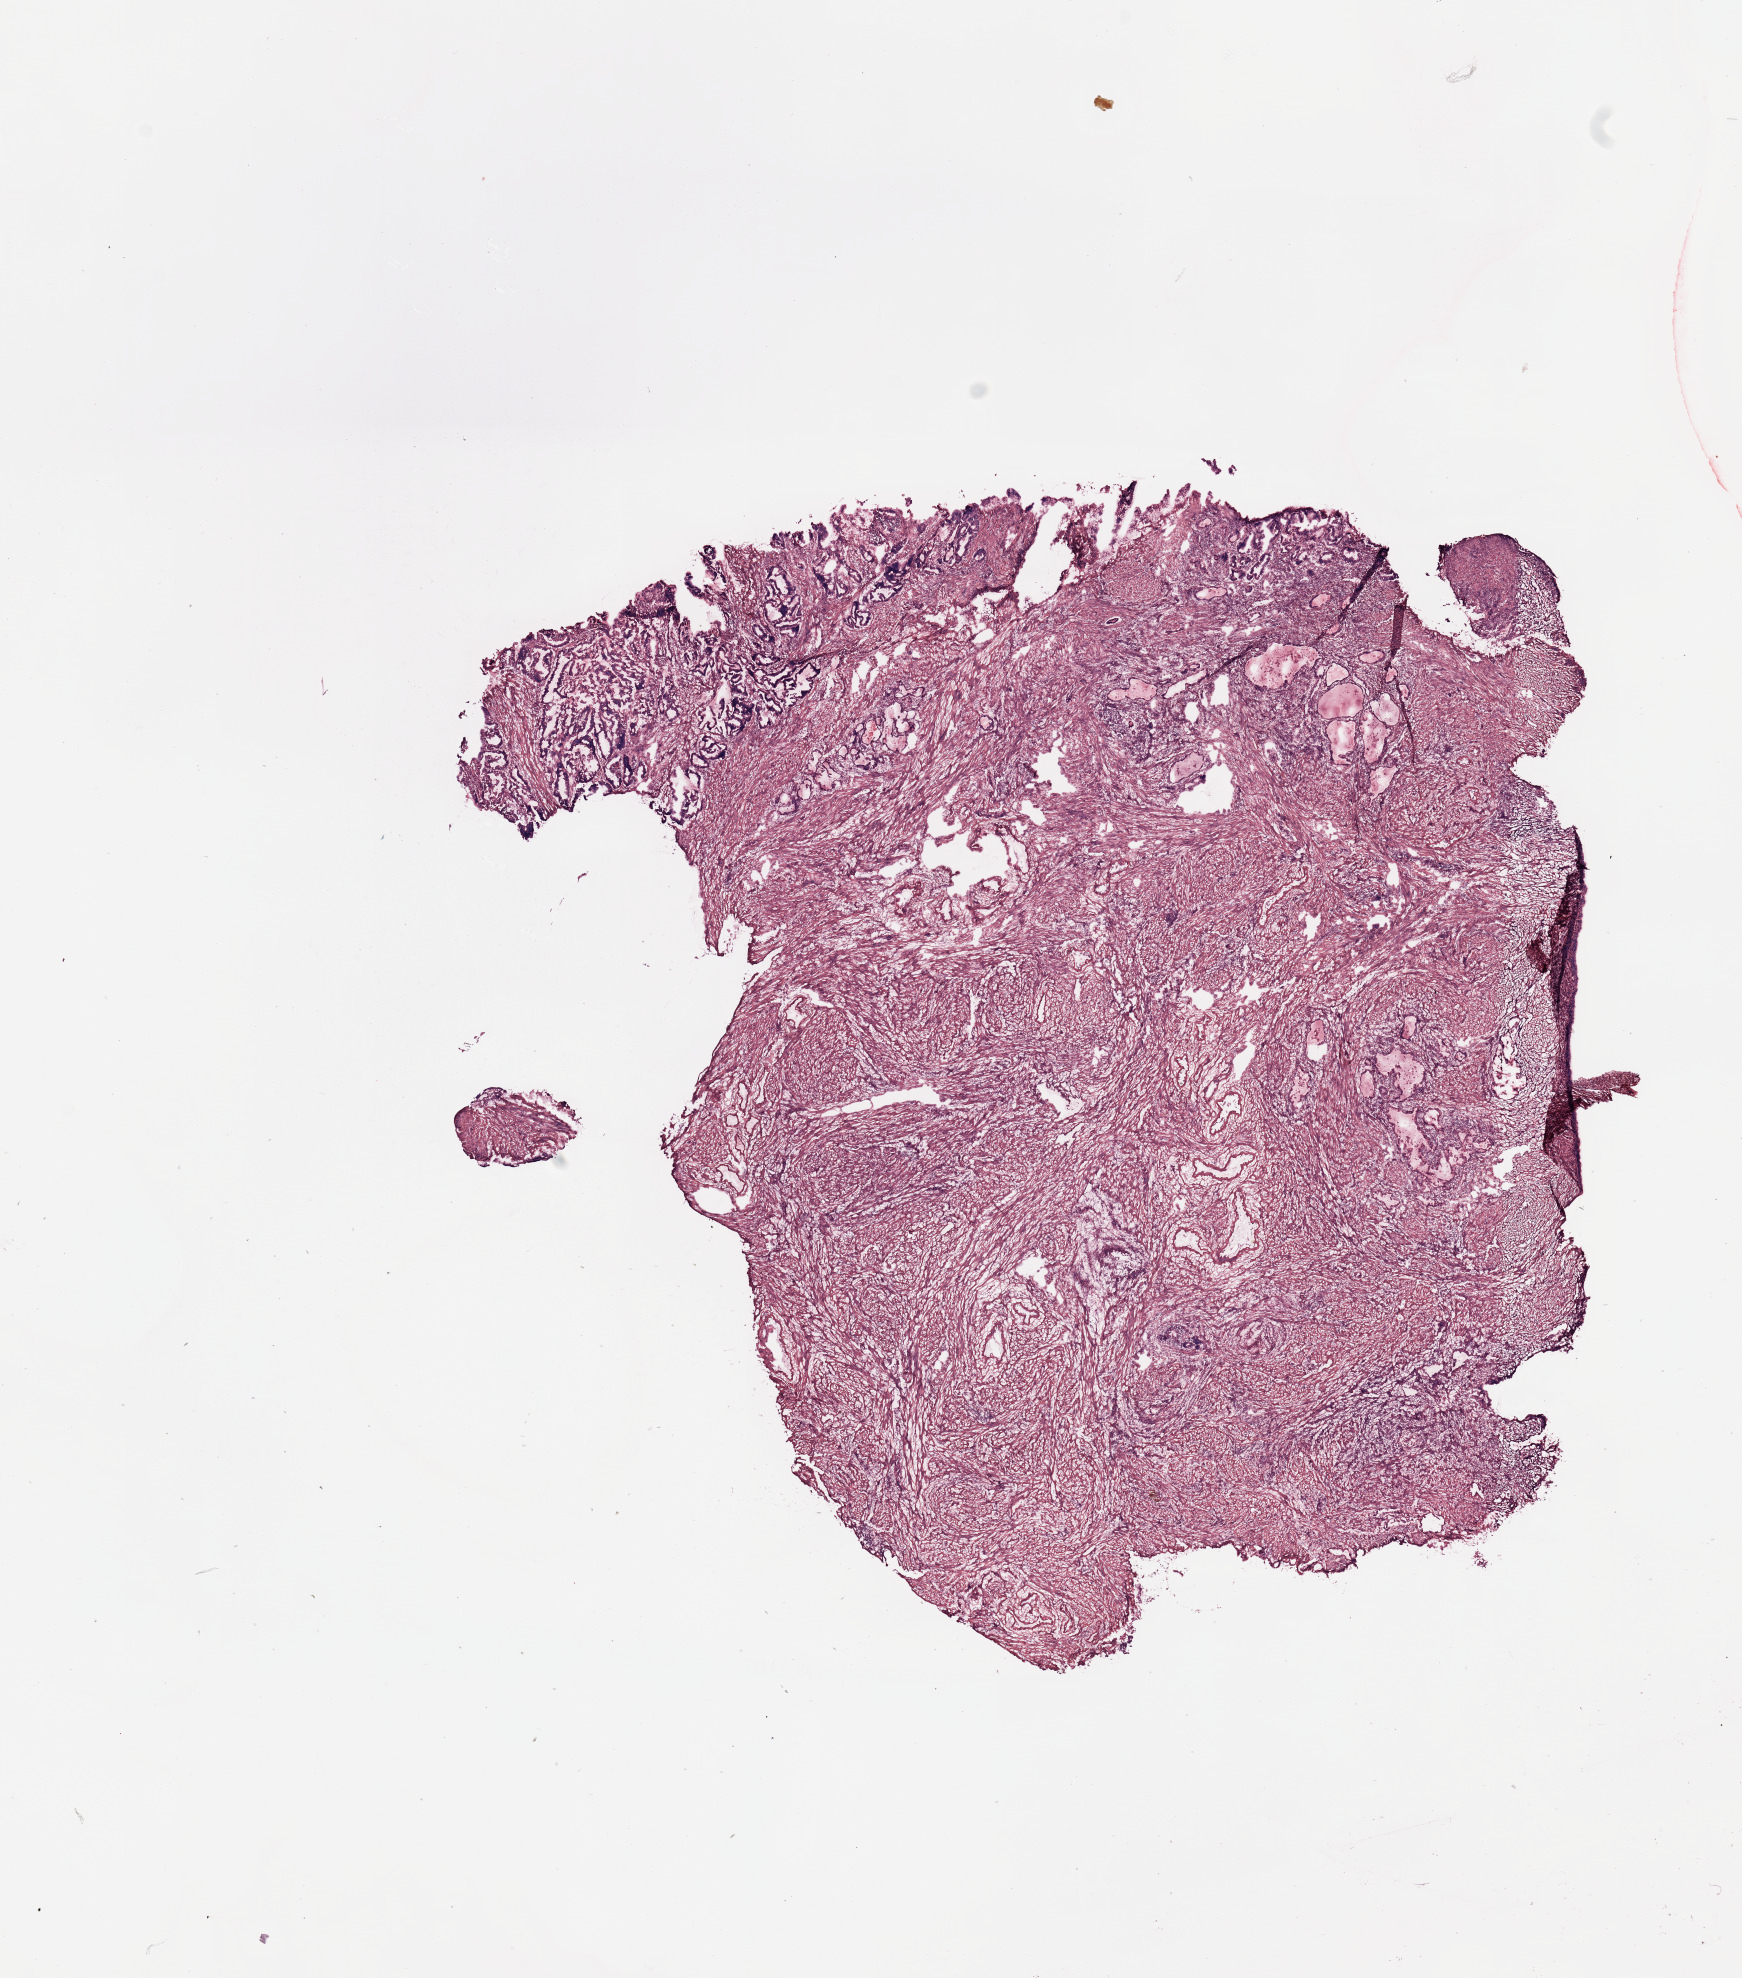
H&E-stained whole-slide image — low-resolution overview of the scanned area, about 13.8 x 15.6 mm; tumour tissue sample, uterus. 68-year-old female patient. Histologic grade: G1 (well differentiated).
AJCC pathologic stage: I. Diagnosis: Endometrioid adenocarcinoma, NOS.